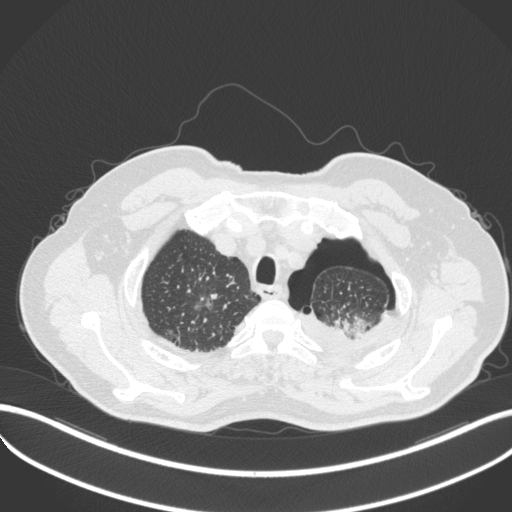
Chest CT, one axial slice. Position 428 of 466 along the scan axis. Reconstruction kernel B31f. 120 kVp. Lung window (W 1500 / L -600 HU). 1 mm slice thickness. 512 × 512 image matrix, field of view 400 × 400 mm. Patient: male, 76 years. Case-level facts recorded for this patient, not image findings: clinical TNM (as recorded): T3 N0 M1b.
Outlined on this slice (bounding box drawn by a radiologist):
- lung tumour (recorded histology: adenocarcinoma): bounding box <340,311,369,337> (left, top, right, bottom; pixels)